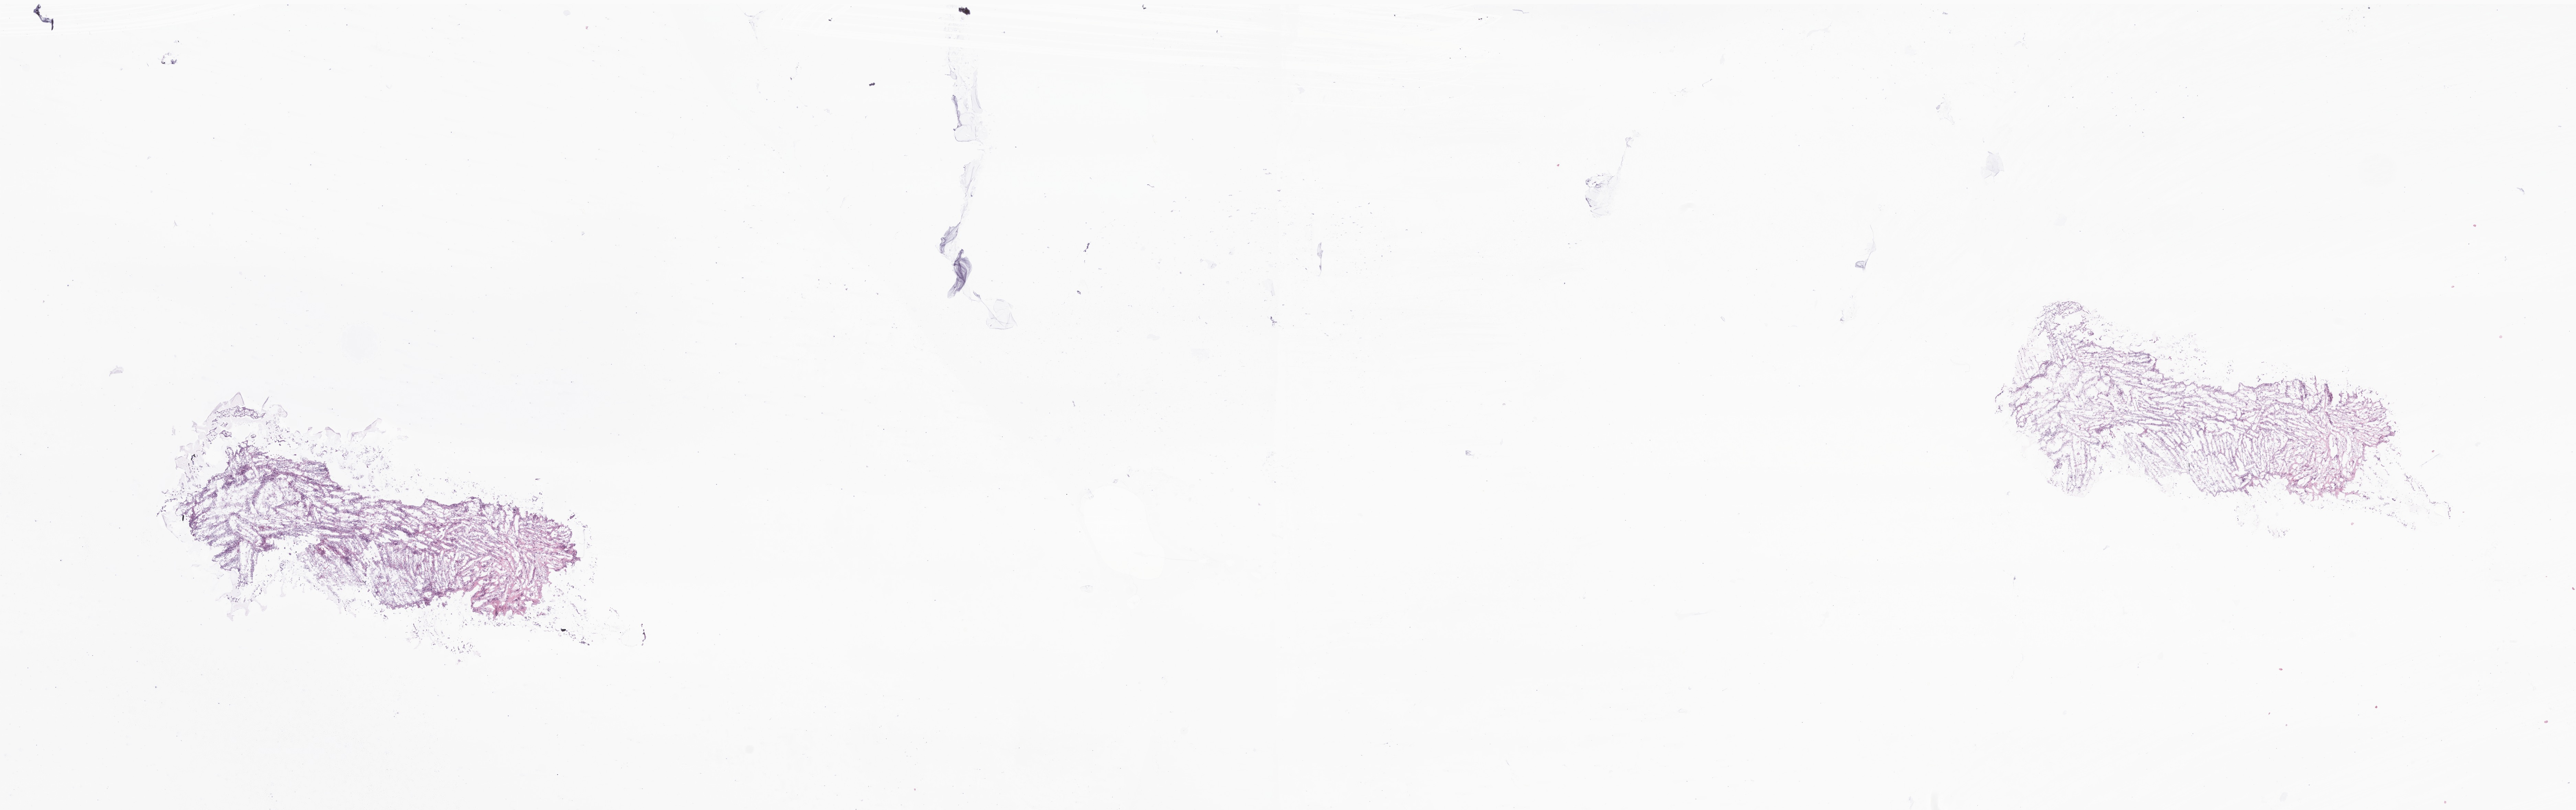
Whole-slide image, H&E stain of tumor tissue from the scrotum, whole scanned area (about 31.6 x 9.9 mm) shown as a low-resolution overview; frozen section (OCT-embedded). Patient male; age 103 months.
- diagnosis: Rhabdomyosarcoma, NOS